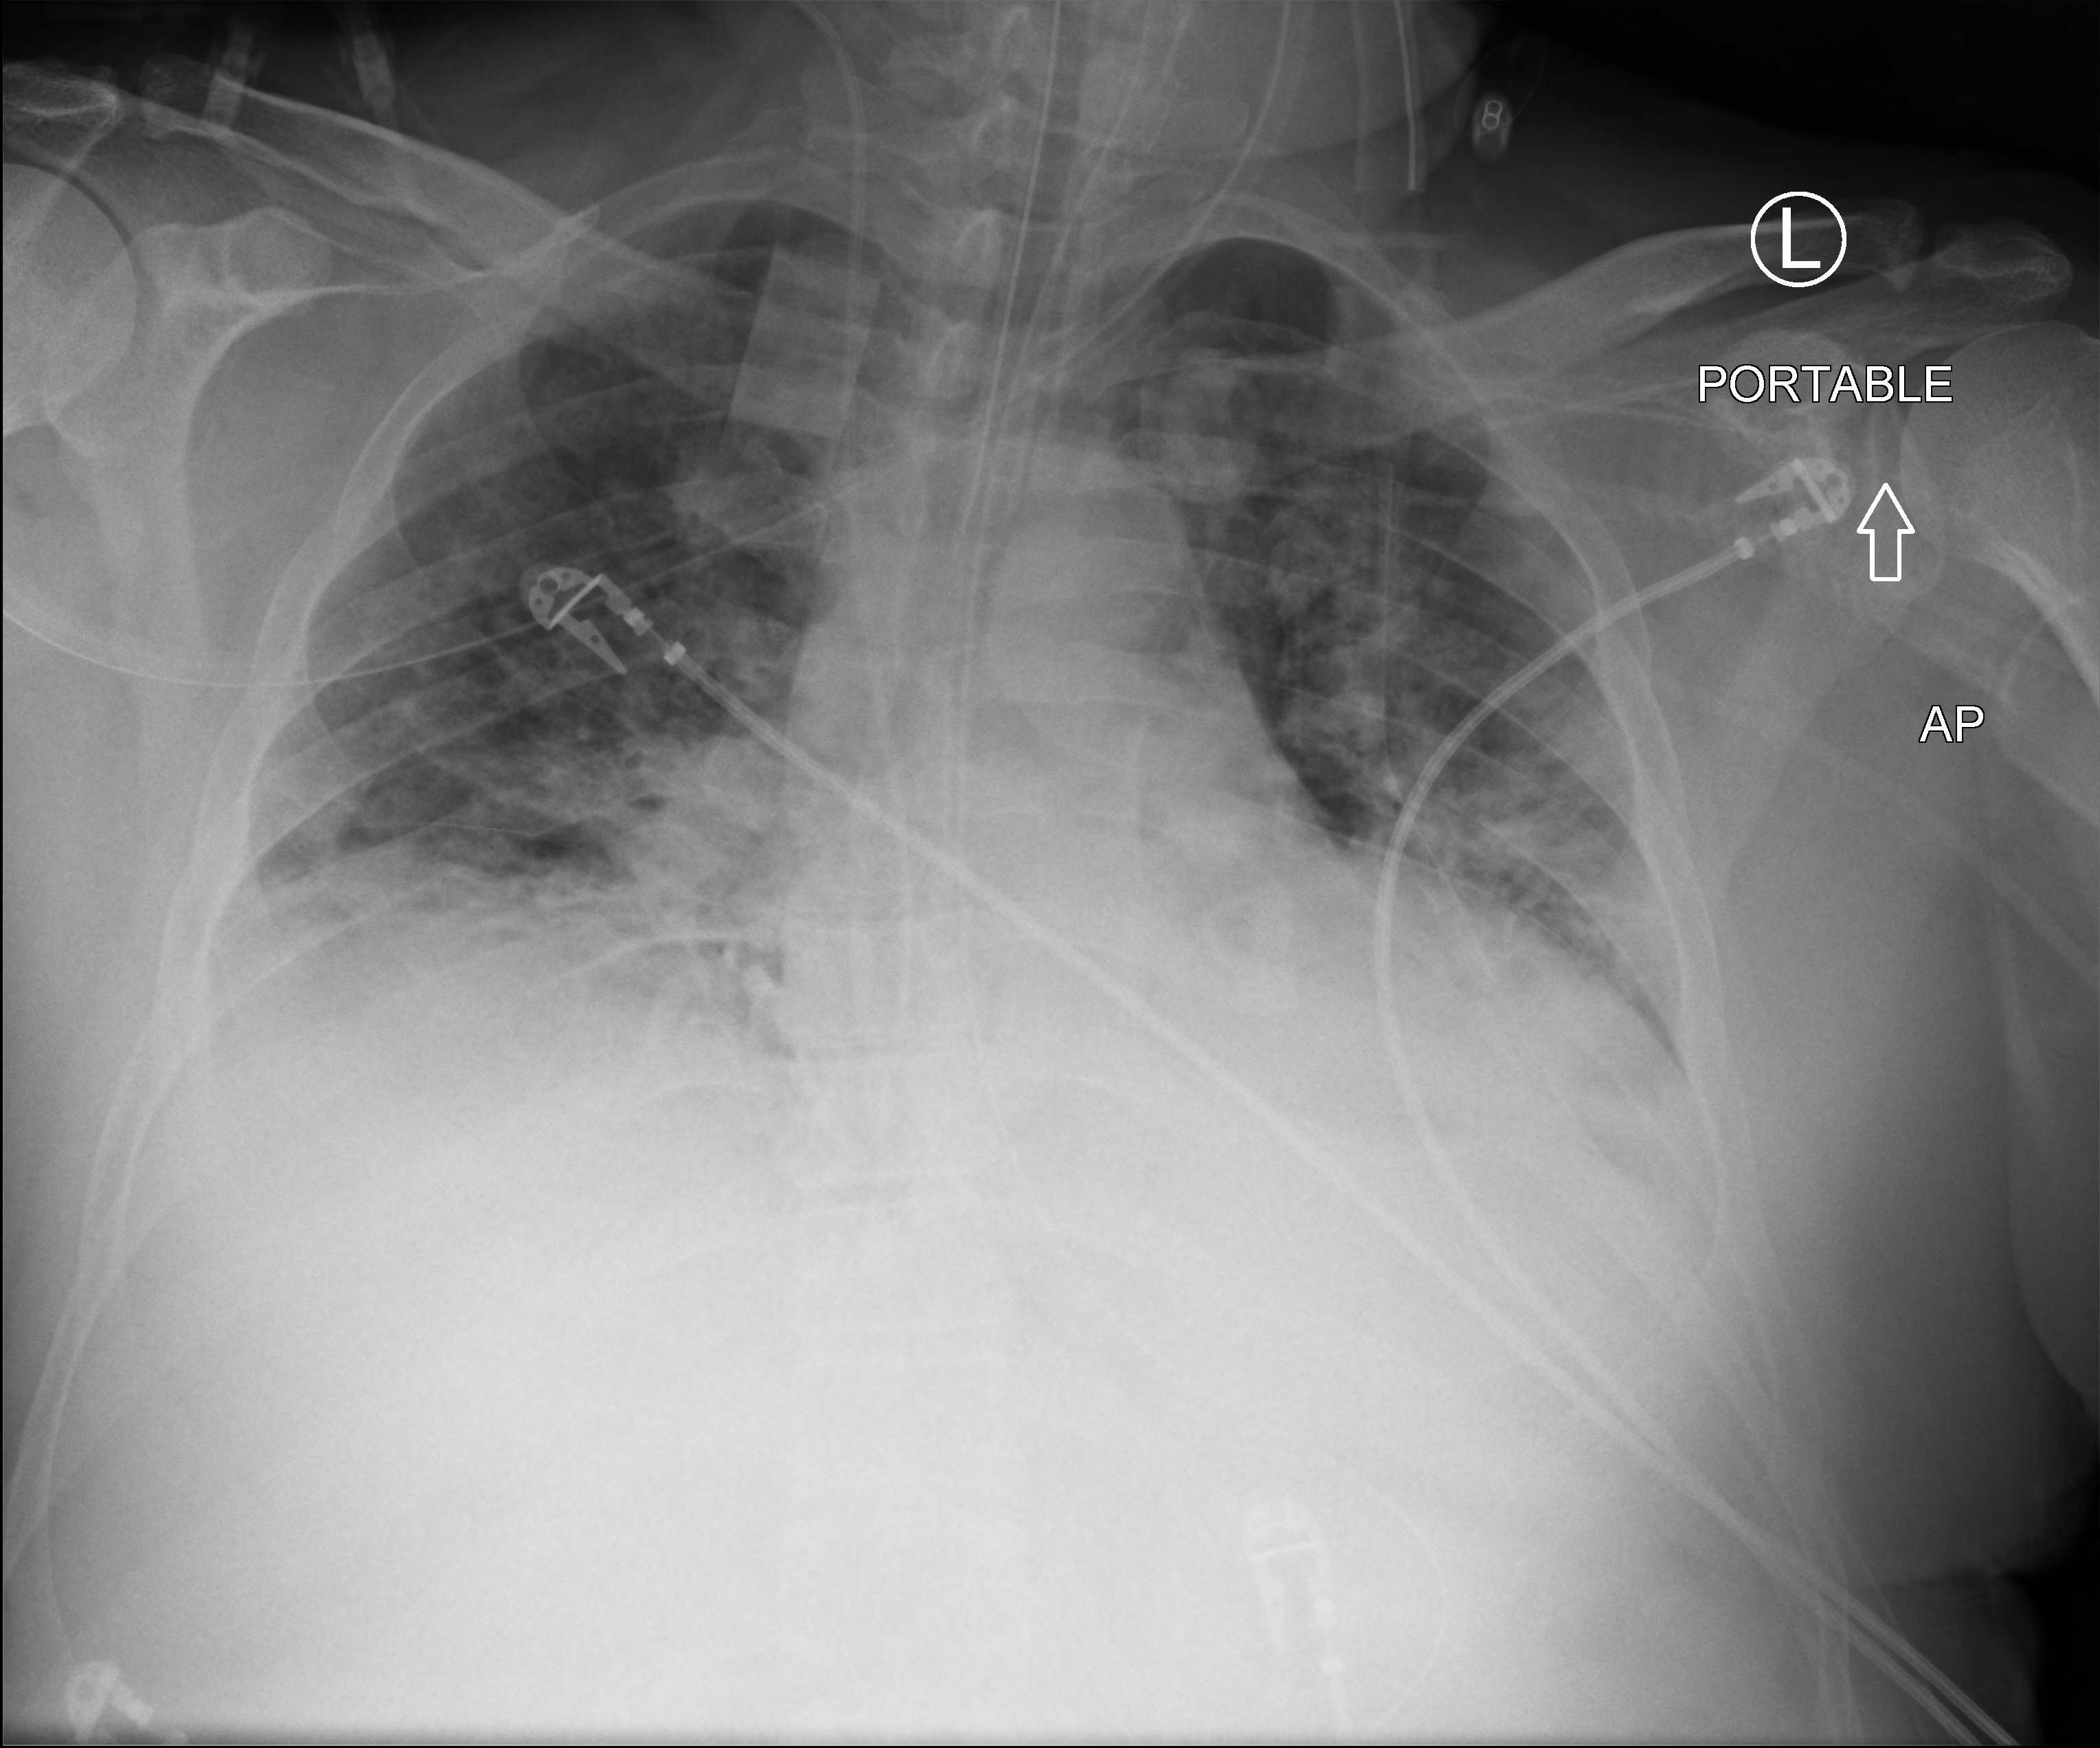
Bedside chest radiograph (computed radiography). Patient hospitalised with COVID-19; male, aged 18–59 years.
Admission-level facts for this patient (not findings on this image; timing relative to this image not recorded): chronic kidney disease (admission record): no; hypertension (admission record): no; mechanically ventilated during this hospital stay: yes.